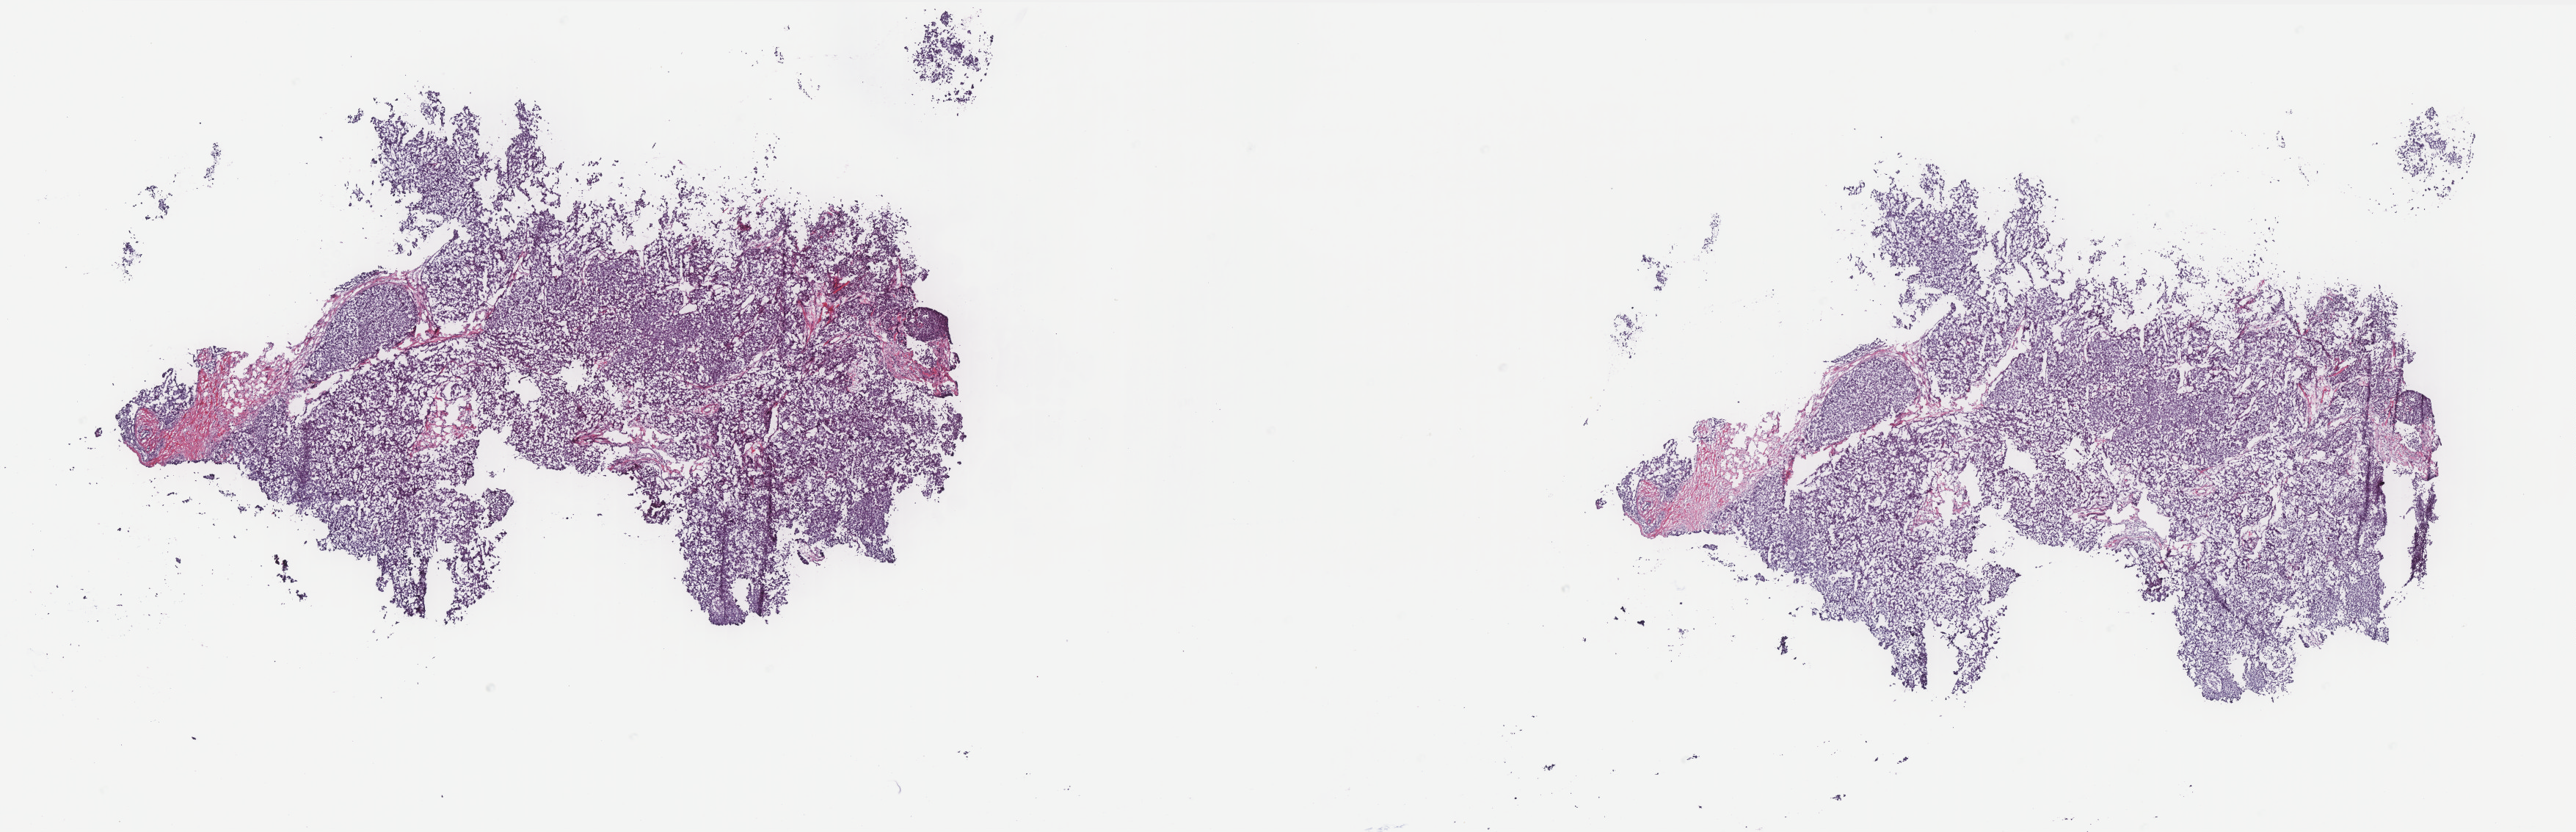
Digitized H&E-stained tissue section (whole slide), a low-resolution overview of the entire scanned area, about 28.1 x 9.1 mm, frozen section from the bottom of the tissue portion, breast, primary tumour sample. Female patient; age at initial diagnosis 63 years. Composition of this section per pathologist review: tumour cells 100%, tumour nuclei 95%, normal cells 0%, stromal cells 0%, necrosis 0%. Infiltration values recorded for this section: lymphocyte infiltration 0%, monocyte infiltration 0%, neutrophil infiltration 0%.
- AJCC pathologic stage: IIA (6th edition)
- laterality: right
- TNM: T2 N0 (i-) M0
- pathologic diagnosis: Infiltrating duct carcinoma, NOS